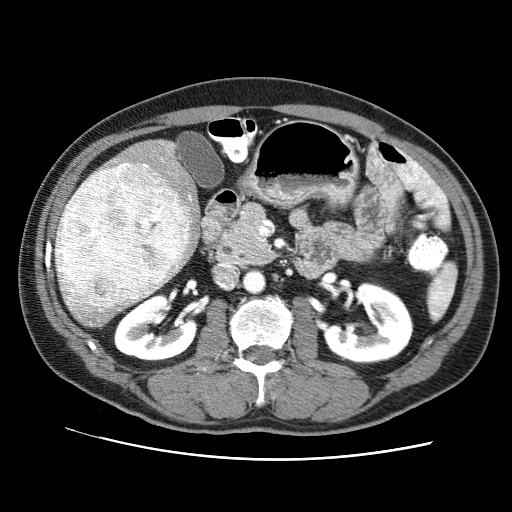
Contrast-enhanced abdominal CT (liver protocol), one axial slice; reconstruction kernel STANDARD; soft-tissue window (W 400 / L 40 HU); 2.5 mm slice thickness; 512 × 512 image matrix. Case-level facts recorded for this patient, not image findings: diagnosis: hepatocellular carcinoma (patient treated with transarterial chemoembolisation; whether this scan precedes or follows treatment is not stated here); TNM stage (as recorded): Stage-II; Child-Pugh class: A; tumour nodularity: multinodular; tumour size: 4.6 cm.
Structures marked on this image (semi-automatic segmentation, software-assisted and operator-edited):
- liver parenchyma outside the tumour (the mass and vessels are separate outlines, so this box may not span the whole liver): bounding box (x1, y1, x2, y2) in pixels: (54, 139, 203, 325)
- mass: (55, 162, 188, 319)
- liver vessels: (169, 194, 191, 270)